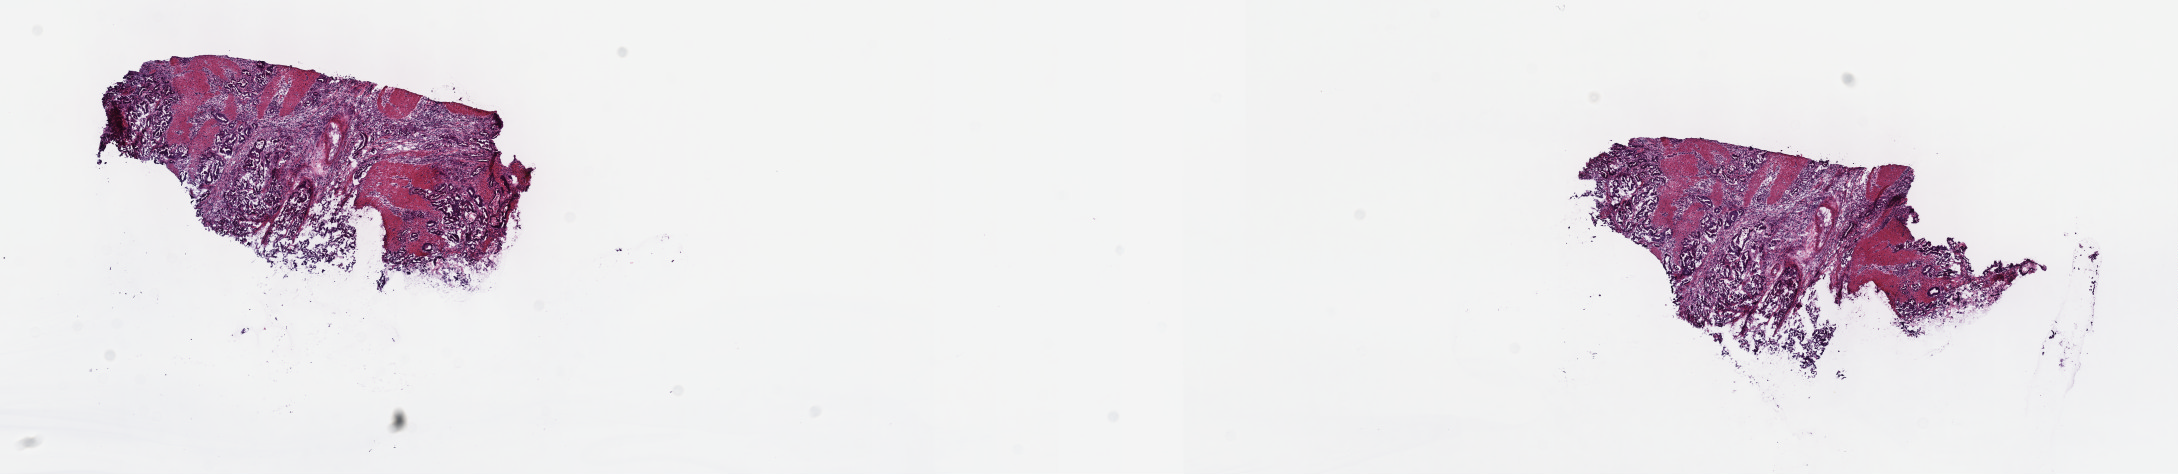
Digitized H&E tissue section (whole slide), a low-resolution overview of the entire scanned area, about 17.6 x 3.8 mm; frozen section; sample: primary tumour, stomach. Male patient; age at initial diagnosis 69 years. Histologic grade: G2 (moderately differentiated). Slide review estimates, as recorded: tumour cells 33%, tumour nuclei 75%, normal cells 0%, stromal cells 60%, necrosis 7%. Infiltration values recorded for this section: lymphocyte infiltration 20%, monocyte infiltration 1%, neutrophil infiltration 2%.
Histologic diagnosis: Adenocarcinoma, intestinal type (gastric antrum). Lymph nodes positive (case pathology): 4 of 31 examined. TNM: T3 N1 M0. AJCC pathologic stage: IIIA (6th edition).